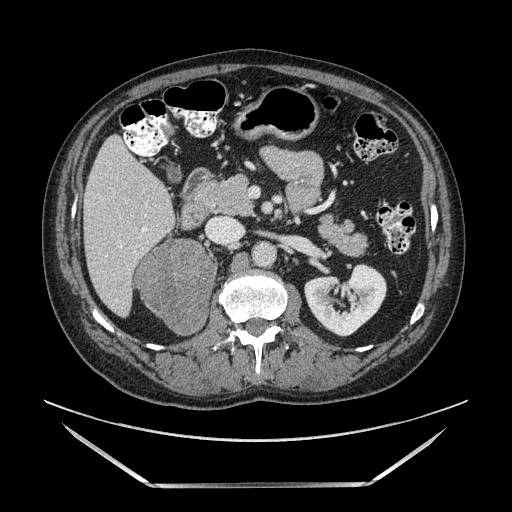
Contrast-enhanced abdominal CT, one axial slice; position 62 of 185 along the scan axis; soft-tissue window (W 400 / L 40 HU); 1.25 mm slice thickness; 512 × 512 image matrix. Male patient. Case-level facts recorded for this patient, not image findings: diagnosis: adrenocortical carcinoma; tumour side: right adrenal; tumour size at pathology: 10.3 cm; Ki-67 index: 20 %; stage (as recorded): 3.
Structures marked on this image (semi-automatic segmentation, software-assisted and operator-edited):
- mass: box from (x=137, y=242) to (x=215, y=332) px